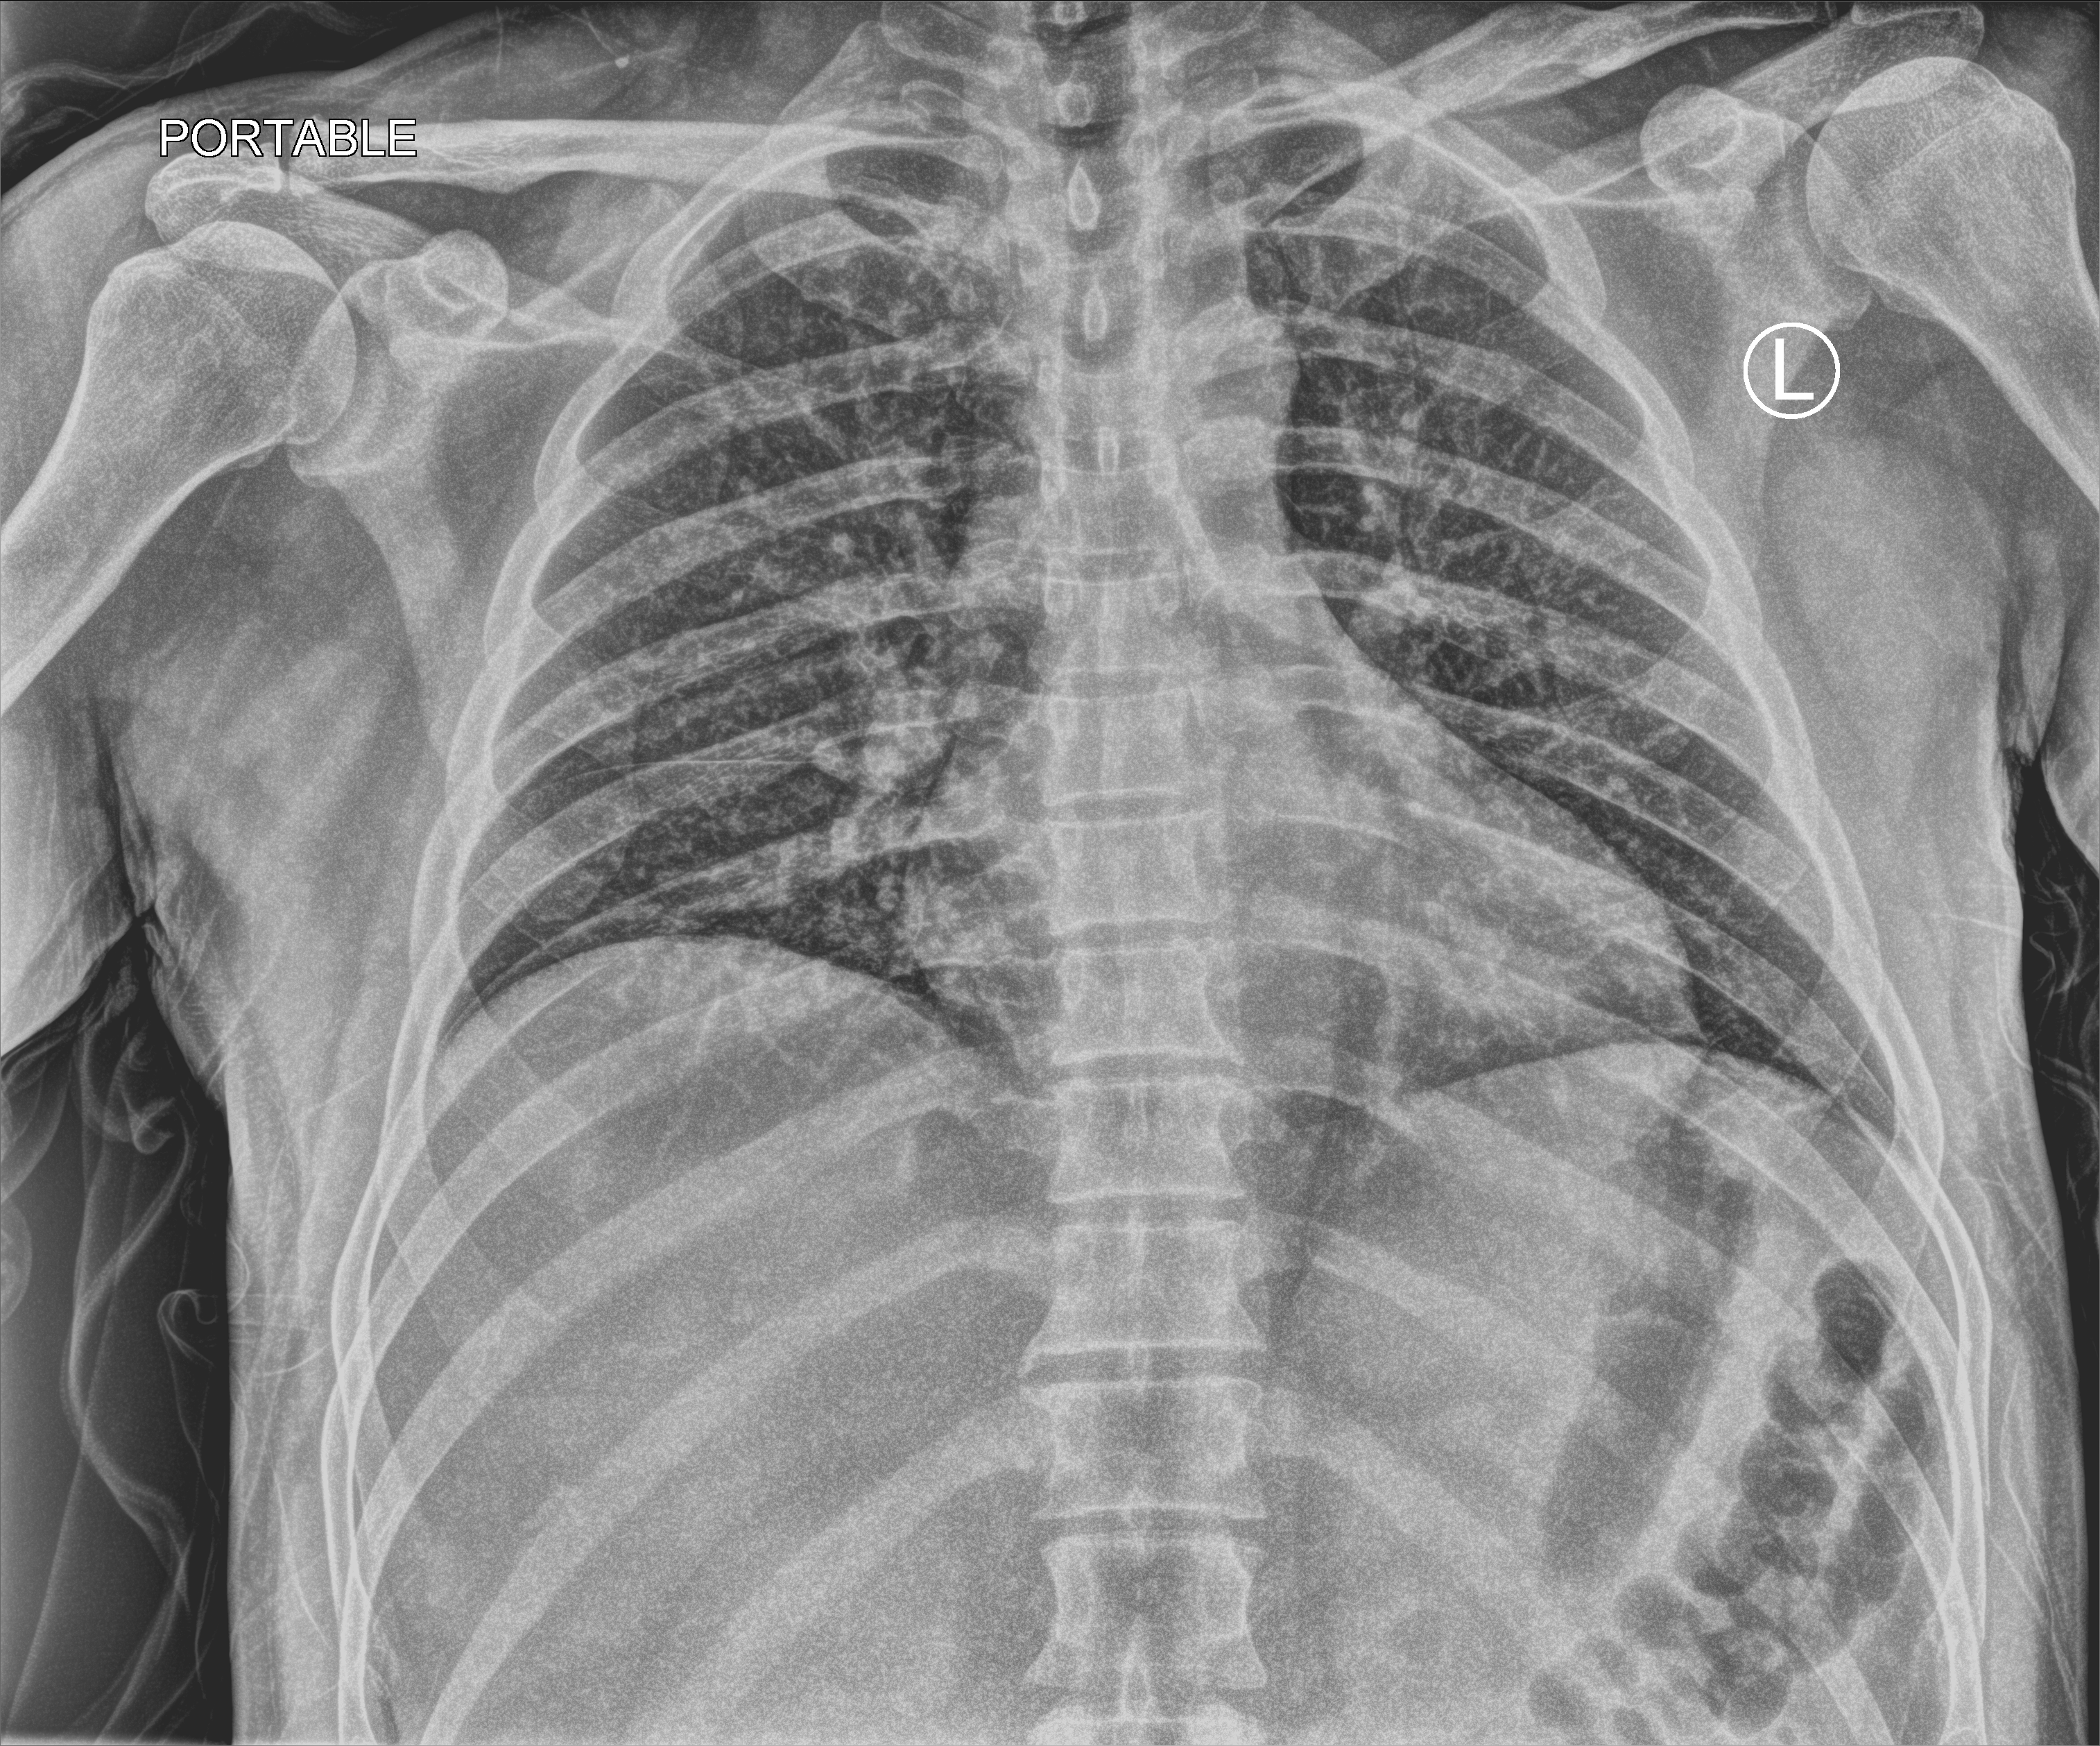
Chest X-ray (portable); anteroposterior (AP) projection. Male patient hospitalised with COVID-19, age 18–59 years.
Admission-level facts for this patient (not findings on this image; timing relative to this image not recorded): COPD (admission record): no.